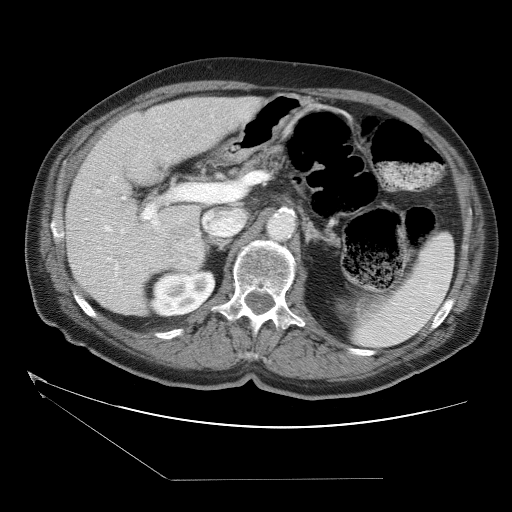
Contrast-enhanced abdominal CT (liver protocol), one axial slice. Position 17 of 38 along the scan axis. 120 kVp. One of 2 acquisitions stored at this slice position. Soft-tissue window (W 400 / L 40 HU). 512 × 512 image matrix, field of view 400 × 400 mm. Case-level facts recorded for this patient, not image findings: diagnosis: hepatocellular carcinoma (patient treated with transarterial chemoembolisation; whether this scan precedes or follows treatment is not stated here); TNM stage (as recorded): Stage-II; Child-Pugh class: A; tumour differentiation: moderately differentiated; tumour nodularity: multinodular.
Outlined on this slice (semi-automatic segmentation, software-assisted and operator-edited):
- liver parenchyma outside the tumour (the mass and vessels are separate outlines, so this box may not span the whole liver): bounding box [x1, y1, x2, y2] px = [66, 96, 262, 314]
- mass: [165, 222, 205, 271]
- liver vessels: [85, 189, 160, 300]